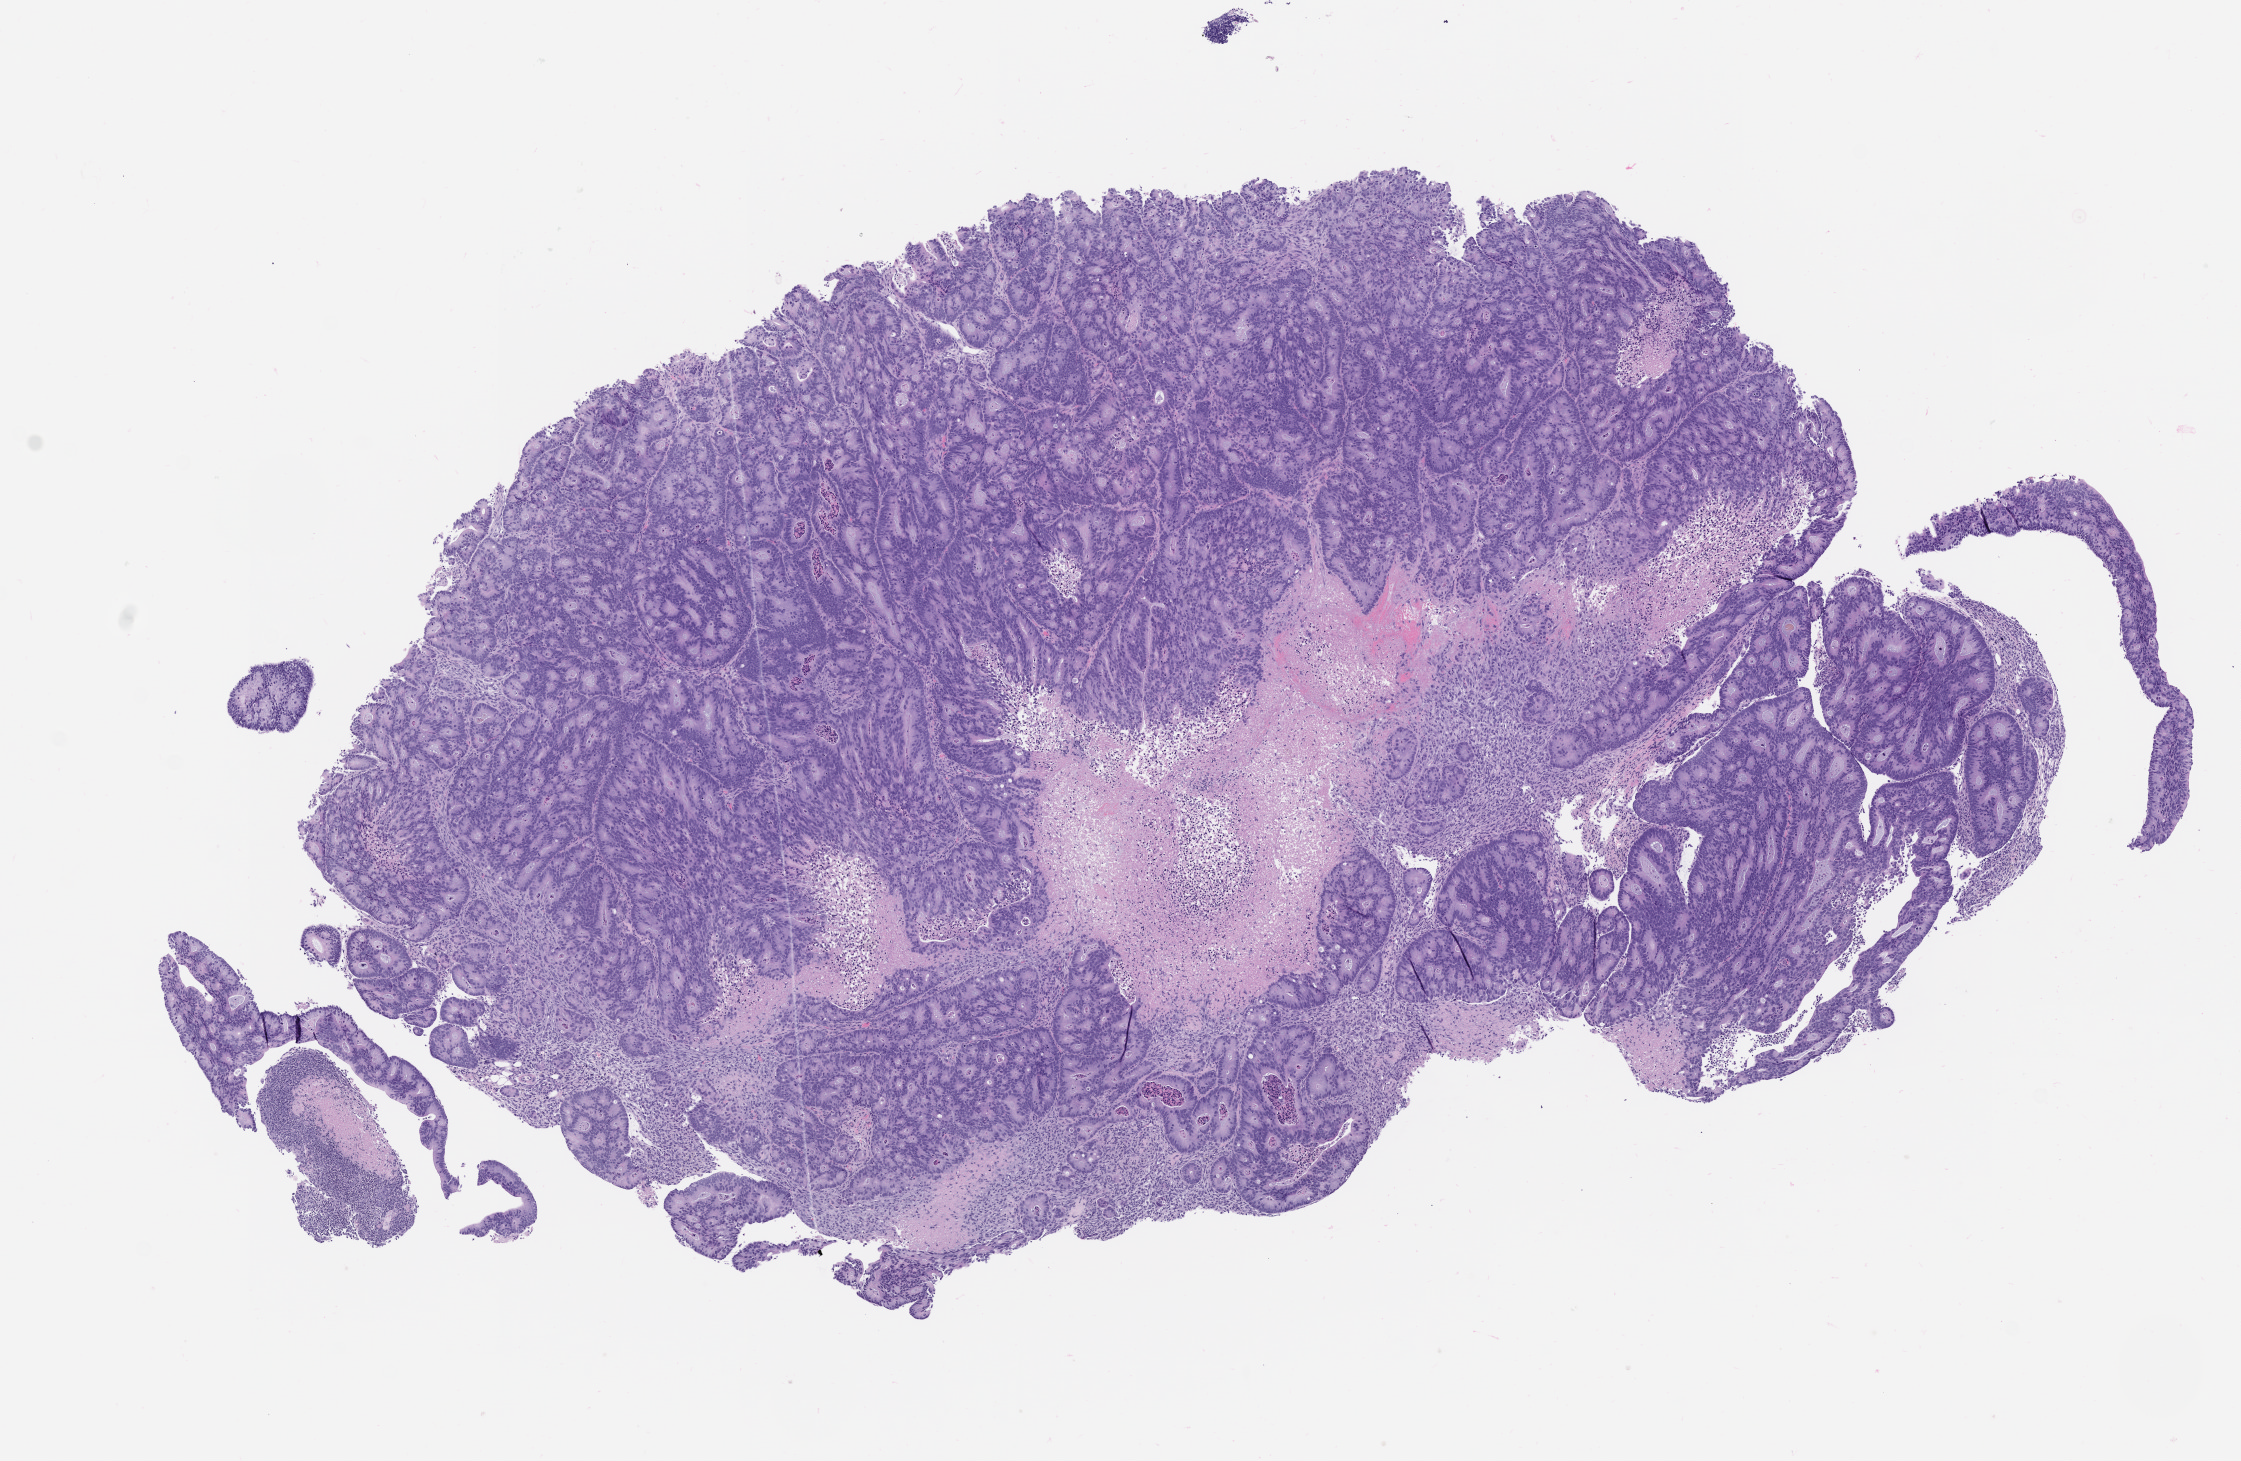
Haematoxylin and eosin whole-slide image of a patient-derived xenograft (PDX) tumor grown in a mouse, passage 1, shown as a low-resolution overview of the whole scanned area (about 9.0 x 5.9 mm). Formalin-fixed, paraffin-embedded (FFPE) tissue. Originating tumor site category: colon.
• originating patient diagnosis: Colon Adenocarcinoma